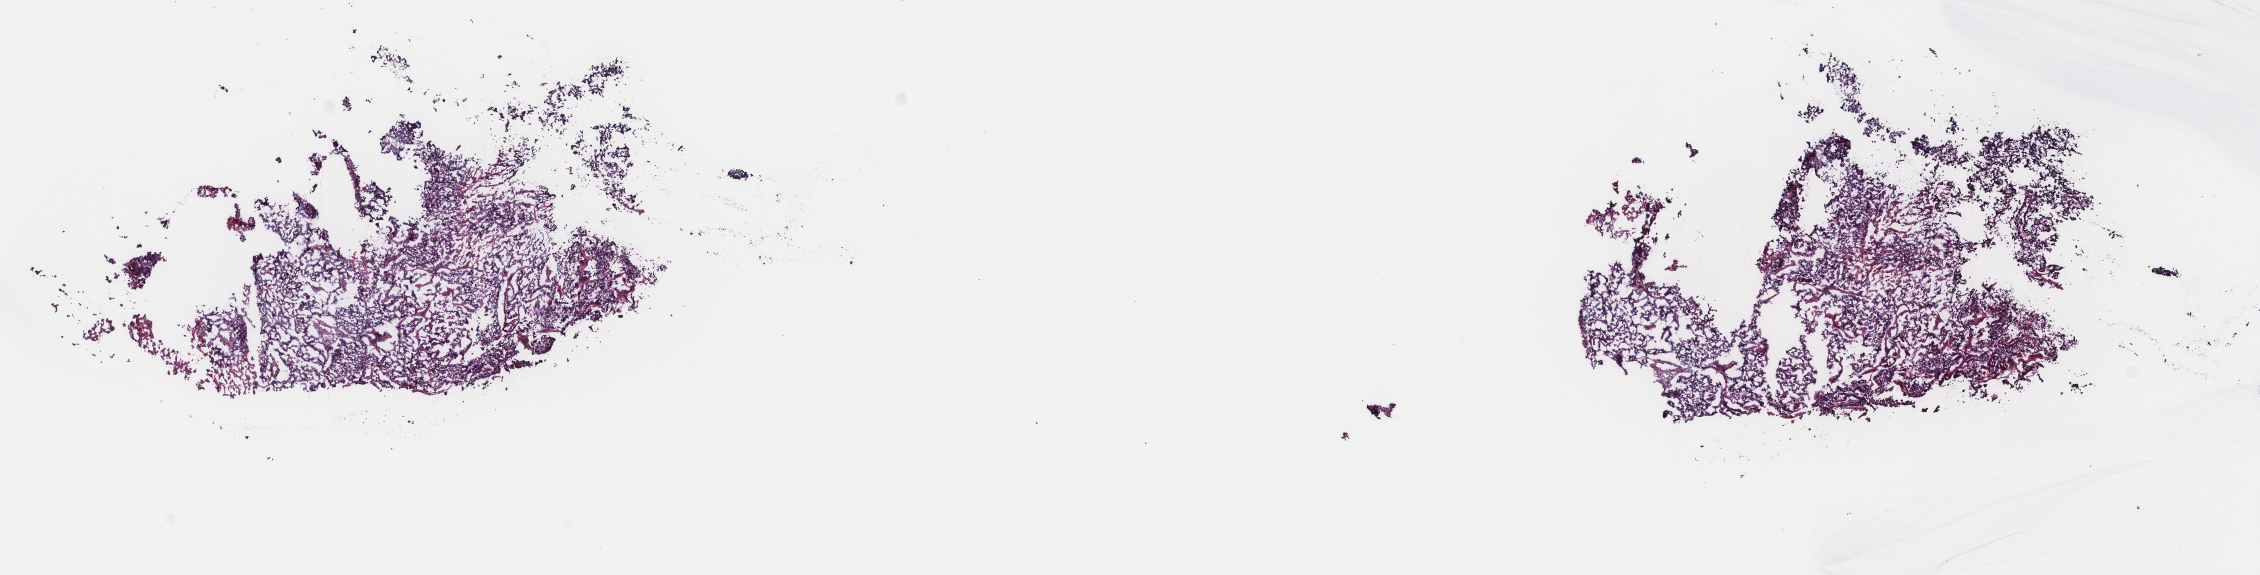
Whole-slide histology image, Hematoxylin and eosin (H&E) stained — low-resolution overview of the scanned area, about 17.9 x 4.6 mm. Frozen section. Primary tumour sample from the uterus. Female patient; age at initial diagnosis 83 years. Pathologist review of this section (percent, as recorded): tumour cells 90%, tumour nuclei 90%, normal cells 0%, stromal cells 10%, necrosis 0%. Infiltration values recorded for this section: lymphocyte infiltration 0%, monocyte infiltration 0%, neutrophil infiltration 0%.
FIGO stage: III. Pathologic diagnosis: Mullerian mixed tumor (endometrium).